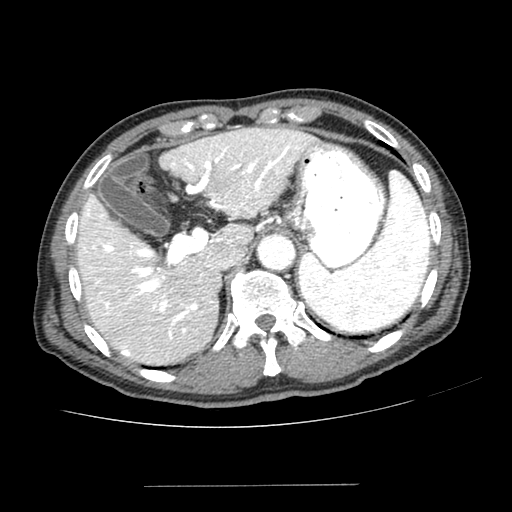
Contrast-enhanced abdominal CT (liver protocol), one axial slice; slice 162 of 187 in the series (ordered by position); reconstruction kernel SOFT; 100 kVp; one of 2 acquisitions stored at this slice position; soft-tissue window (W 400 / L 40 HU); 512 × 512 image matrix, field of view 360 × 360 mm. From the clinical record (not read from this slice): diagnosis: hepatocellular carcinoma (patient treated with transarterial chemoembolisation; whether this scan precedes or follows treatment is not stated here); TNM stage (as recorded): Stage-I; Child-Pugh class: A; tumour differentiation: poorly differentiated; tumour nodularity: uninodular.
Outlined on this slice (semi-automatic segmentation, software-assisted and operator-edited):
- liver parenchyma outside the tumour (the mass and vessels are separate outlines, so this box may not span the whole liver): bounding box (x1, y1, x2, y2) in pixels: (78, 128, 310, 364)
- liver vessels: (84, 136, 300, 356)